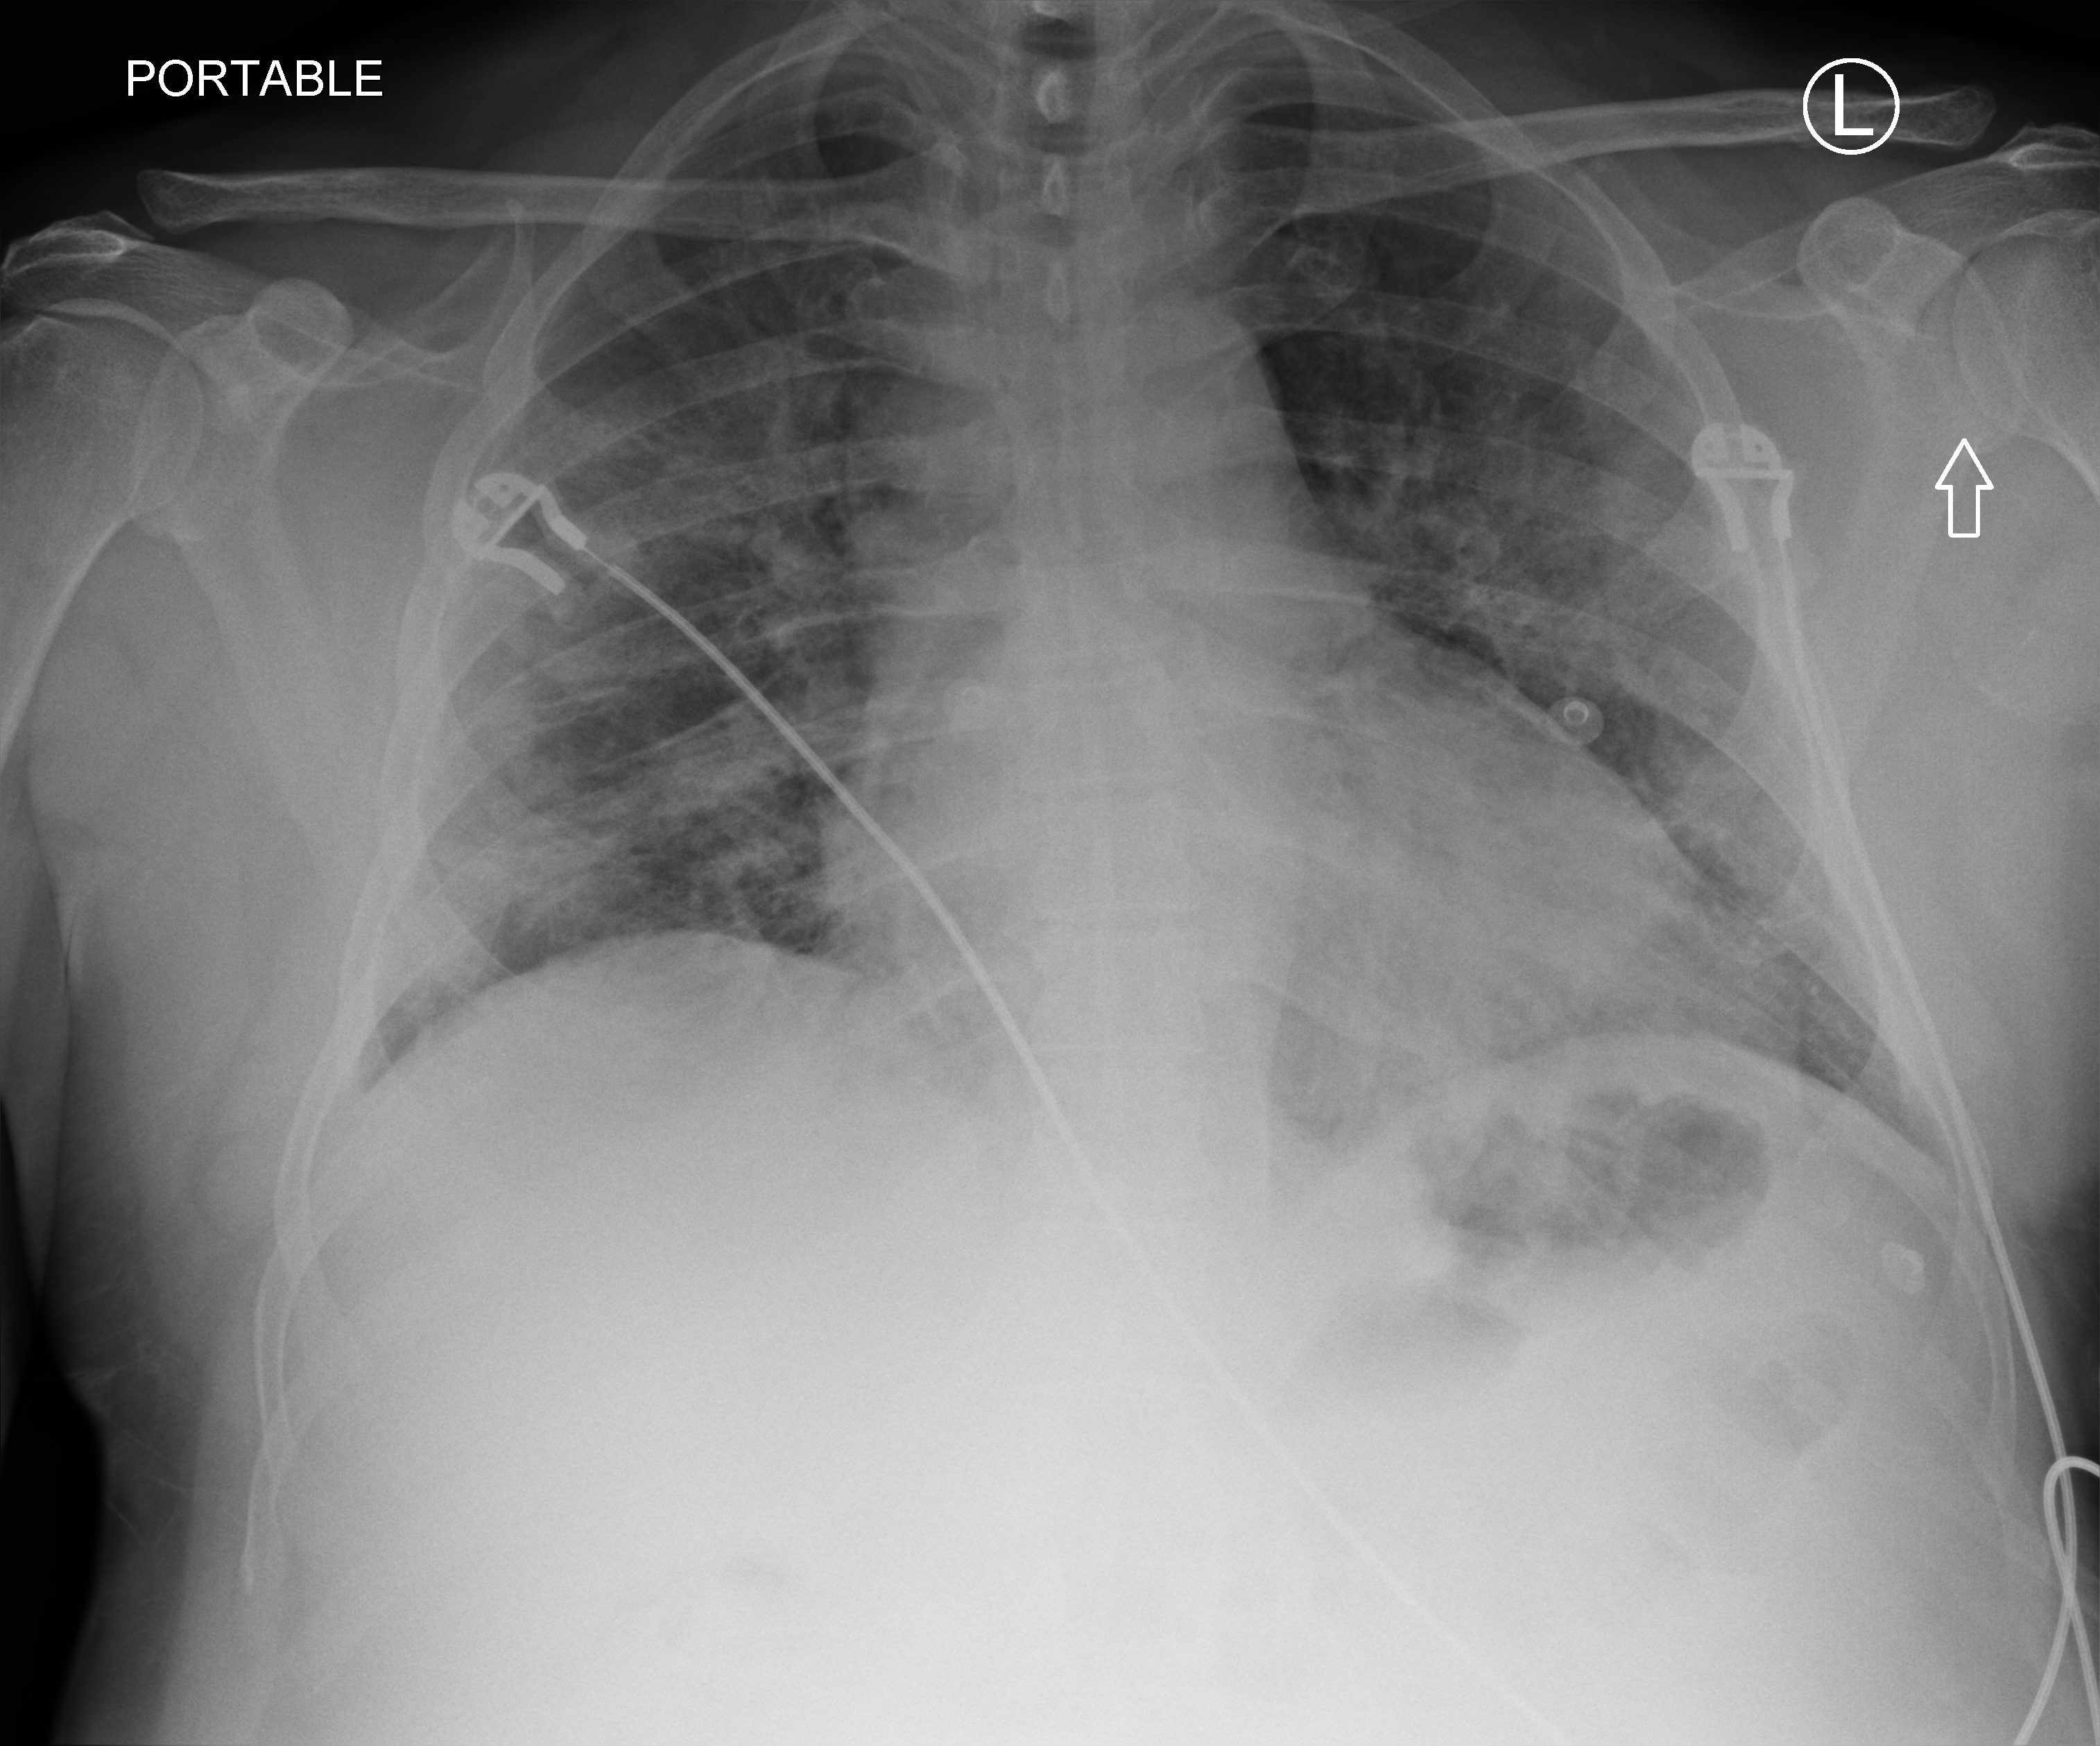
Bedside chest radiograph (computed radiography); anteroposterior (AP) projection. Male patient hospitalised with COVID-19, age 18–59 years.
Hospital-stay facts (about this admission, not read from this image; timing relative to this image not recorded):
- mechanically ventilated during this hospital stay: no
- admitted to intensive care during this hospital stay: no